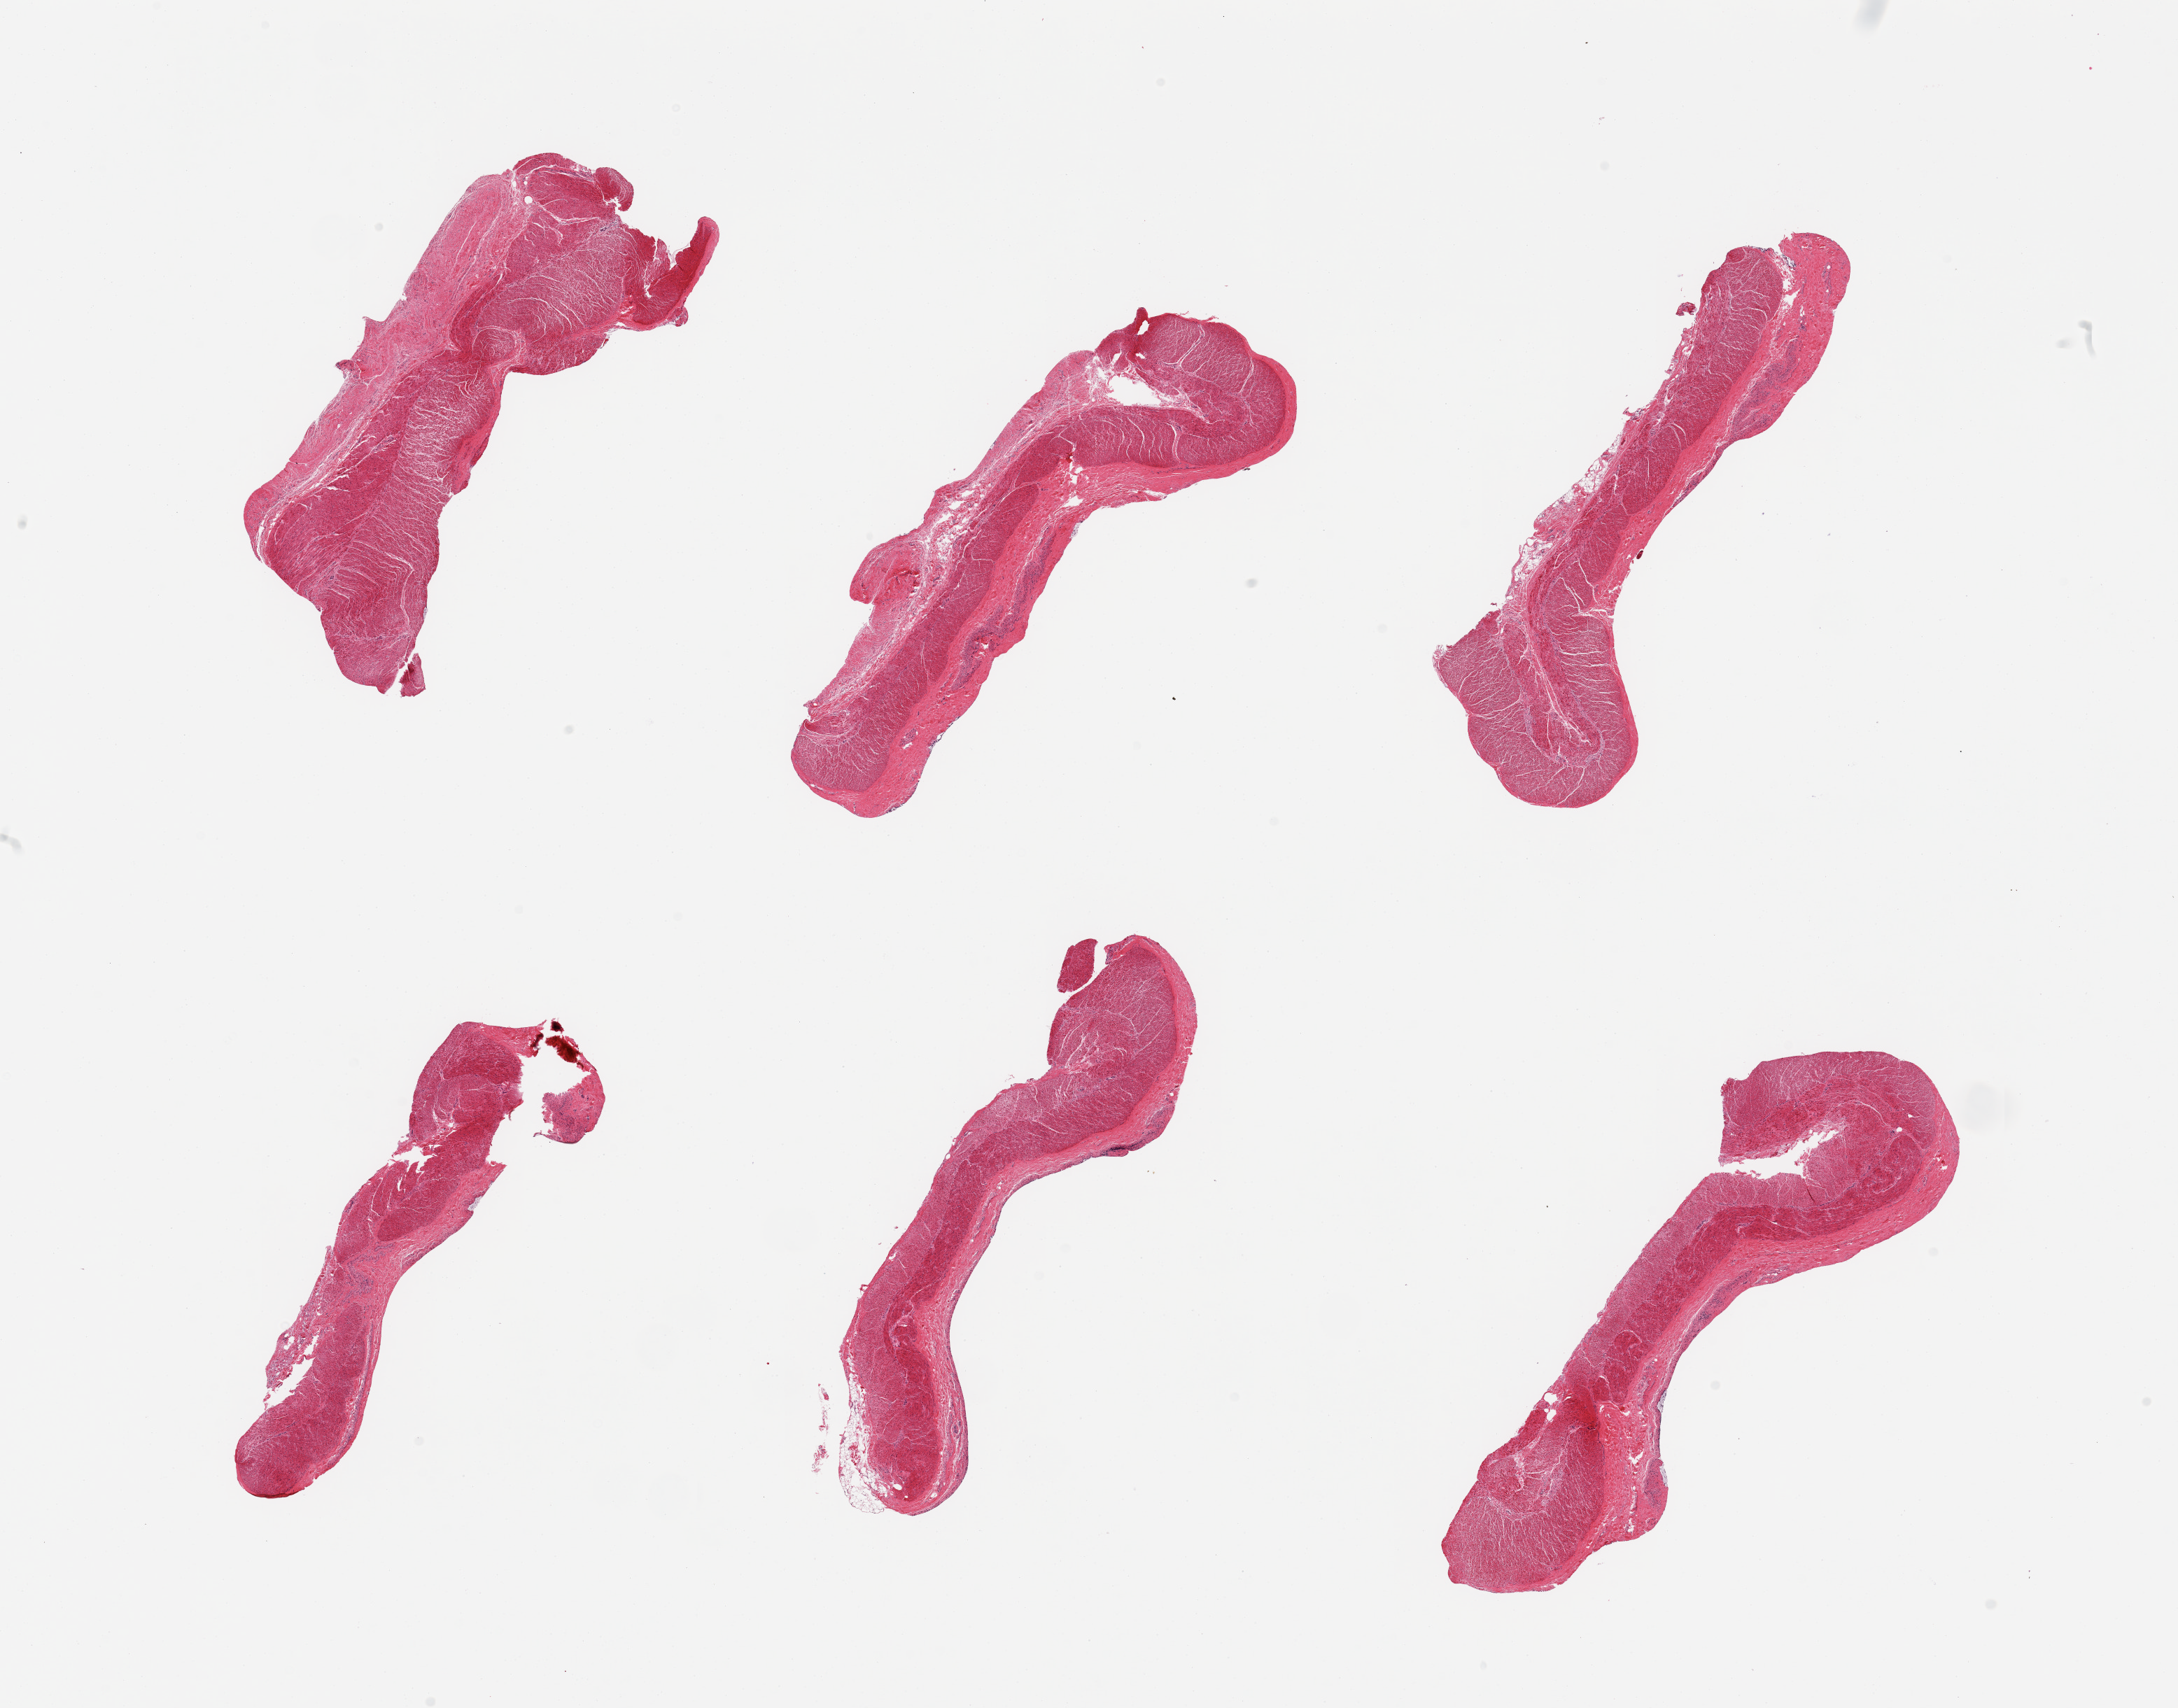
Whole-slide image, H&E stain, brightfield — a low-resolution overview of the entire scanned area, about 24.6 x 19.3 mm. PAXgene-fixed paraffin-embedded (PFPE) section. Target tissue: sigmoid colon. Donor tissue sample. Female donor.
Reviewer comment on this tissue sample: 6 pieces, confirmed muscularis.